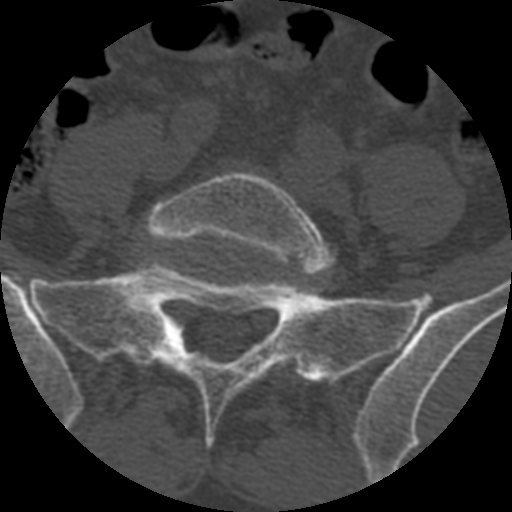
CT including the spine, one axial slice; slice 243 of 399 in the series (ordered by position); reconstruction kernel STANDARD; 120 kVp; bone window (W 1800 / L 400 HU); 1.25 mm slice thickness; 512 × 512 image matrix, field of view 160 × 160 mm. Patient age 71 years. From the clinical record (not read from this slice): primary cancer: prostate.
Annotated regions visible in this slice (semi-automatically segmented with operator editing):
- L5 vertebra: bounding box <144,171,335,273> (left, top, right, bottom; pixels)